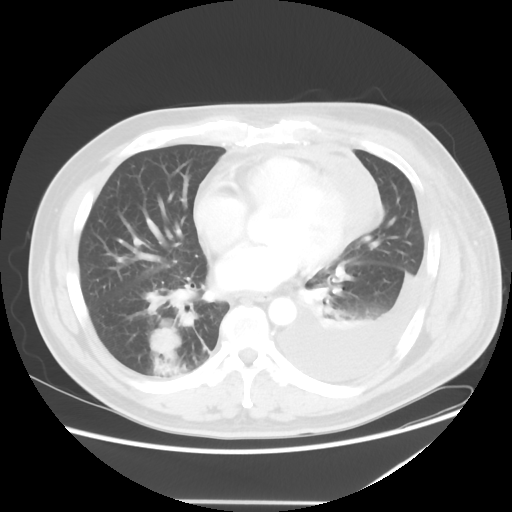
Chest CT, one axial slice; slice 21 of 52 in the series (ordered by position); reconstruction kernel STANDARD; lung window (W 1500 / L -600 HU); 5 mm slice thickness; 512 × 512 image matrix, field of view 405 × 405 mm. Male patient, age 42 years. From the clinical record (not read from this slice): clinical TNM (as recorded): T2 N1 M1.
Outlined on this slice (rectangle marked by the reading radiologist):
- lung tumour (recorded histology: adenocarcinoma): bounding box (x1, y1, x2, y2) in pixels: (147, 327, 186, 359)